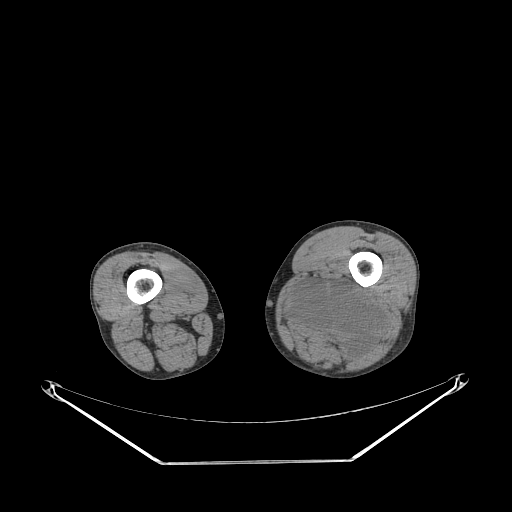
CT of an extremity soft-tissue mass (from a PET/CT study), one axial slice; slice 214 of 267 in the series (ordered by position); reconstruction kernel STANDARD; soft-tissue window (W 400 / L 40 HU); 512 × 512 image matrix, field of view 500 × 500 mm. Male patient. Case-level facts recorded for this patient, not image findings: histological type: undifferentiated pleomorphic liposarcoma; grade: high; site of the primary tumour: left thigh.
Structures marked on this image (expert contour drawn on MRI and transferred to this co-registered scan by the dataset authors):
- gross tumour volume including surrounding oedema: bounding box (x1, y1, x2, y2) in pixels: (286, 272, 382, 359)
- gross tumour volume (mass): (290, 283, 380, 355)